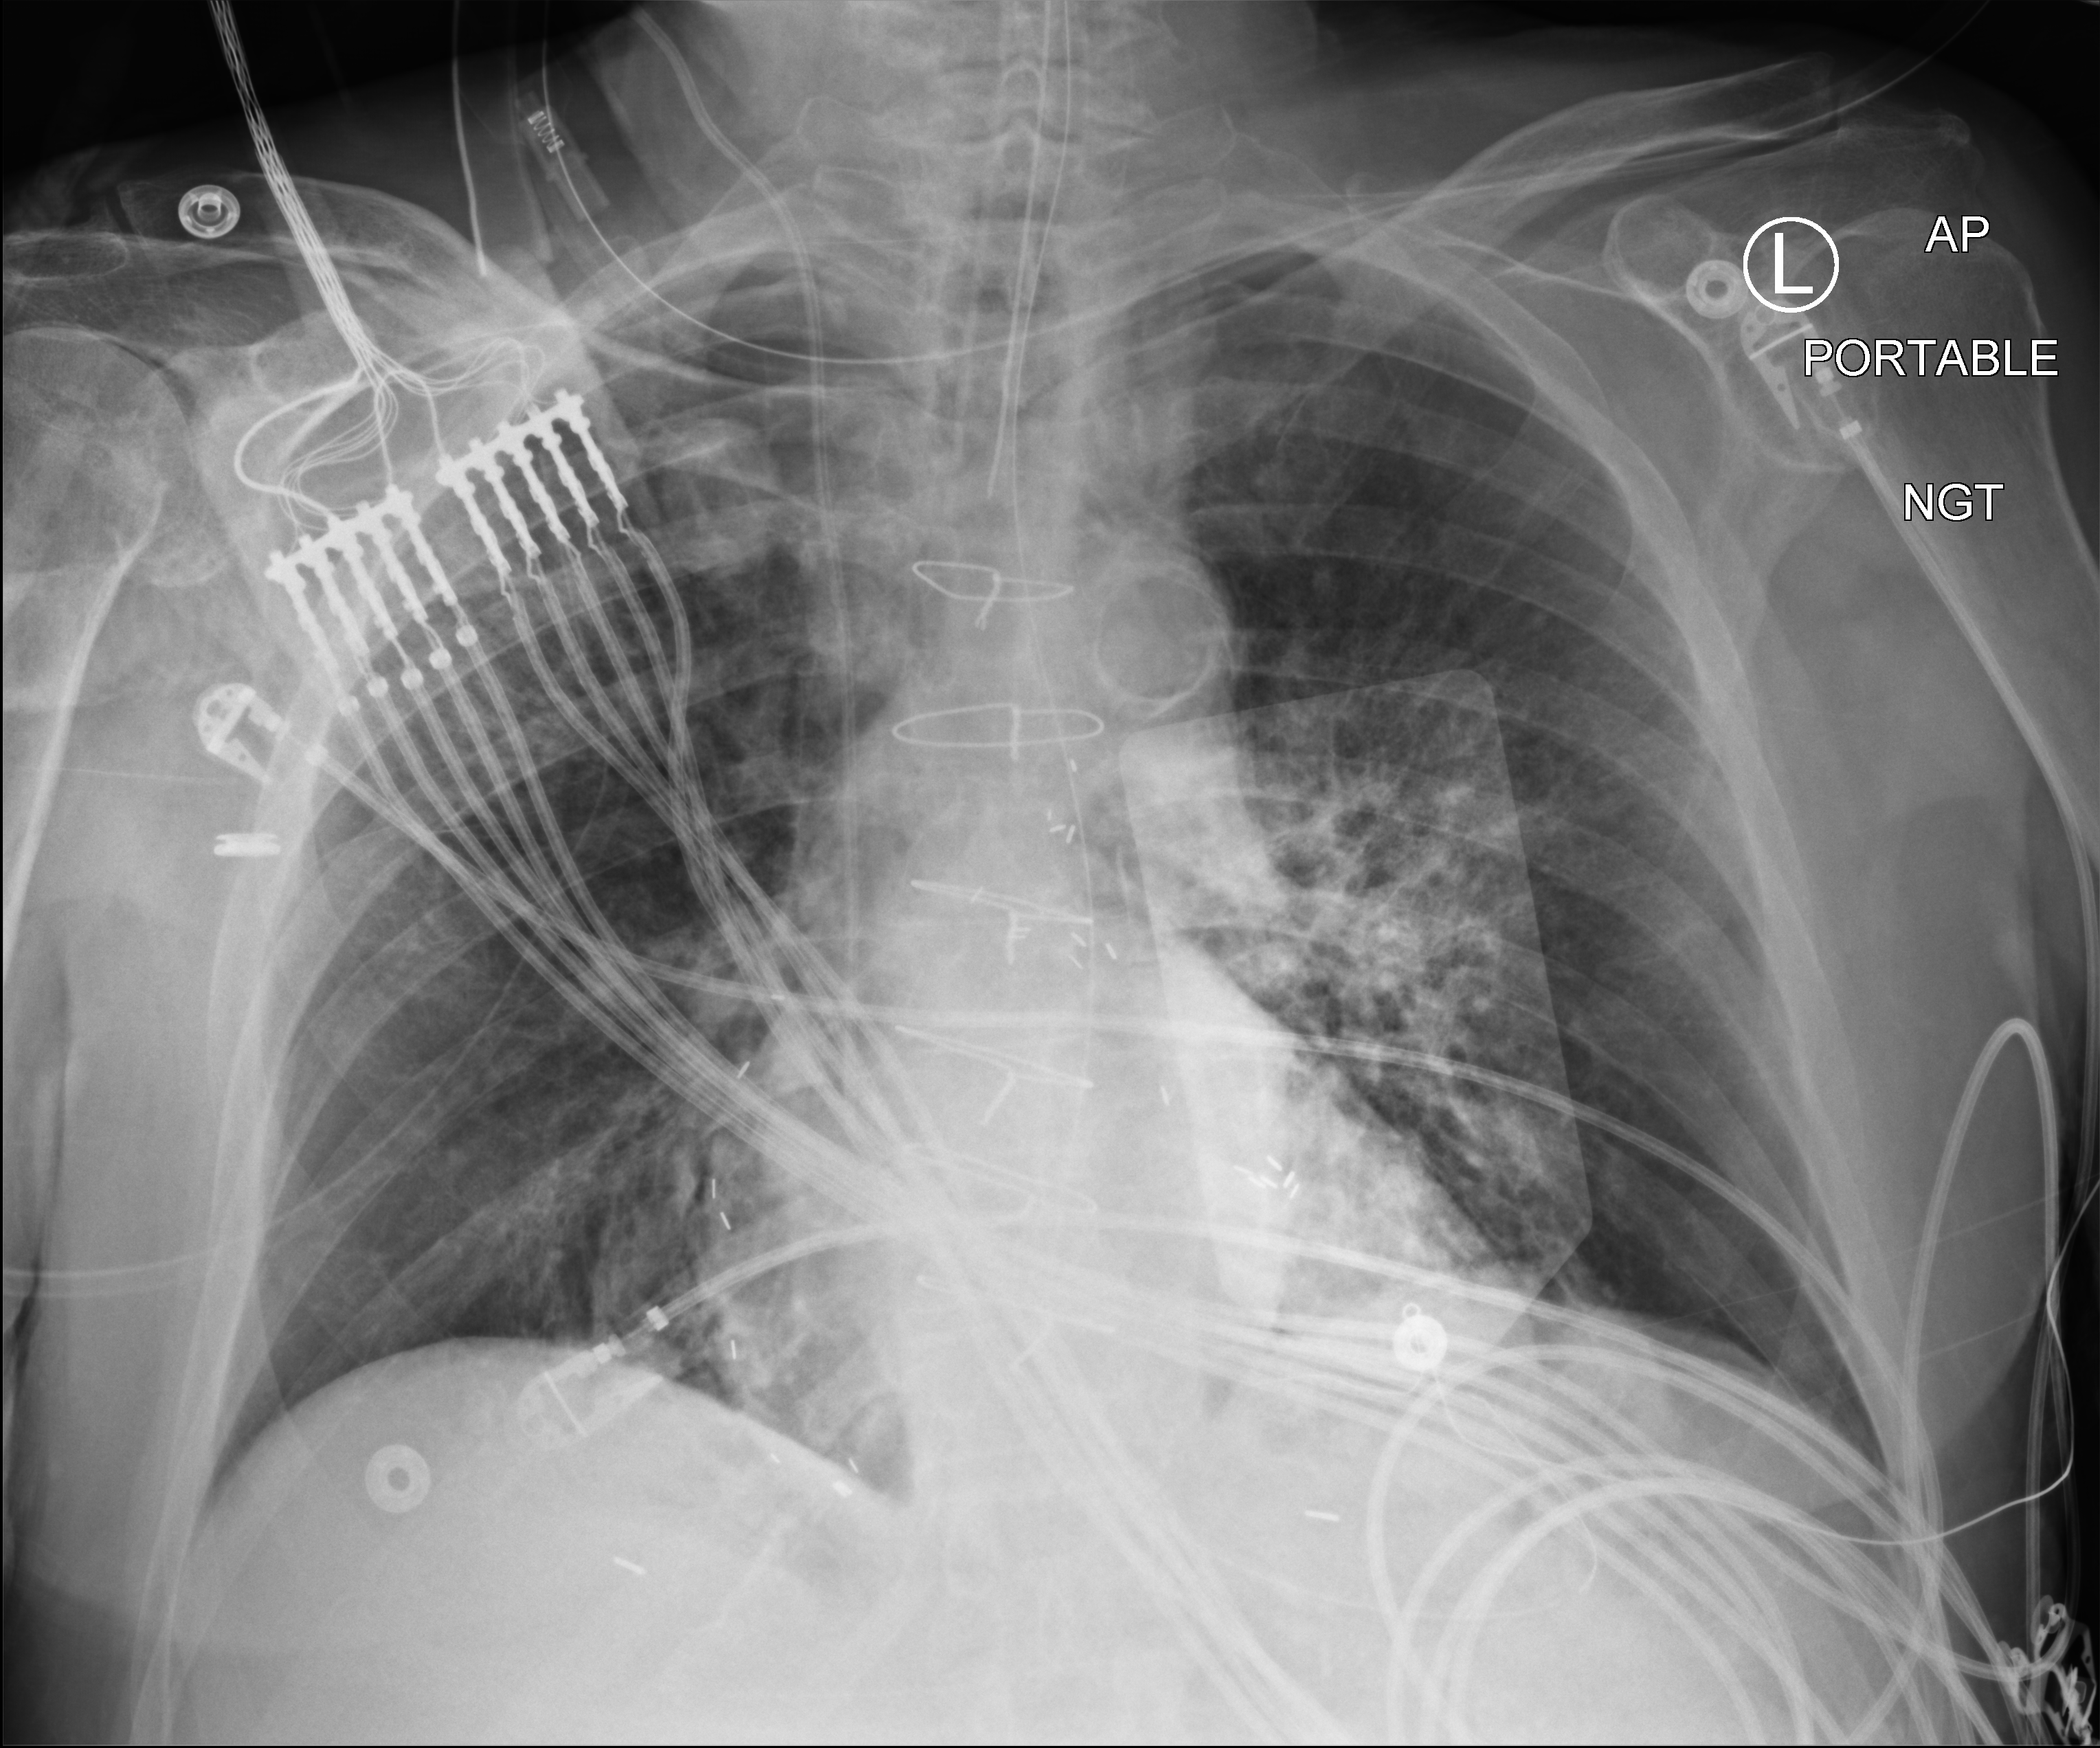
Portable chest radiograph; anteroposterior (AP) projection. Male patient hospitalised with COVID-19, age 75–90 years.
Admission-level facts for this patient (not findings on this image; timing relative to this image not recorded): admitted to intensive care during this hospital stay: yes; length of hospital stay: 10 days.